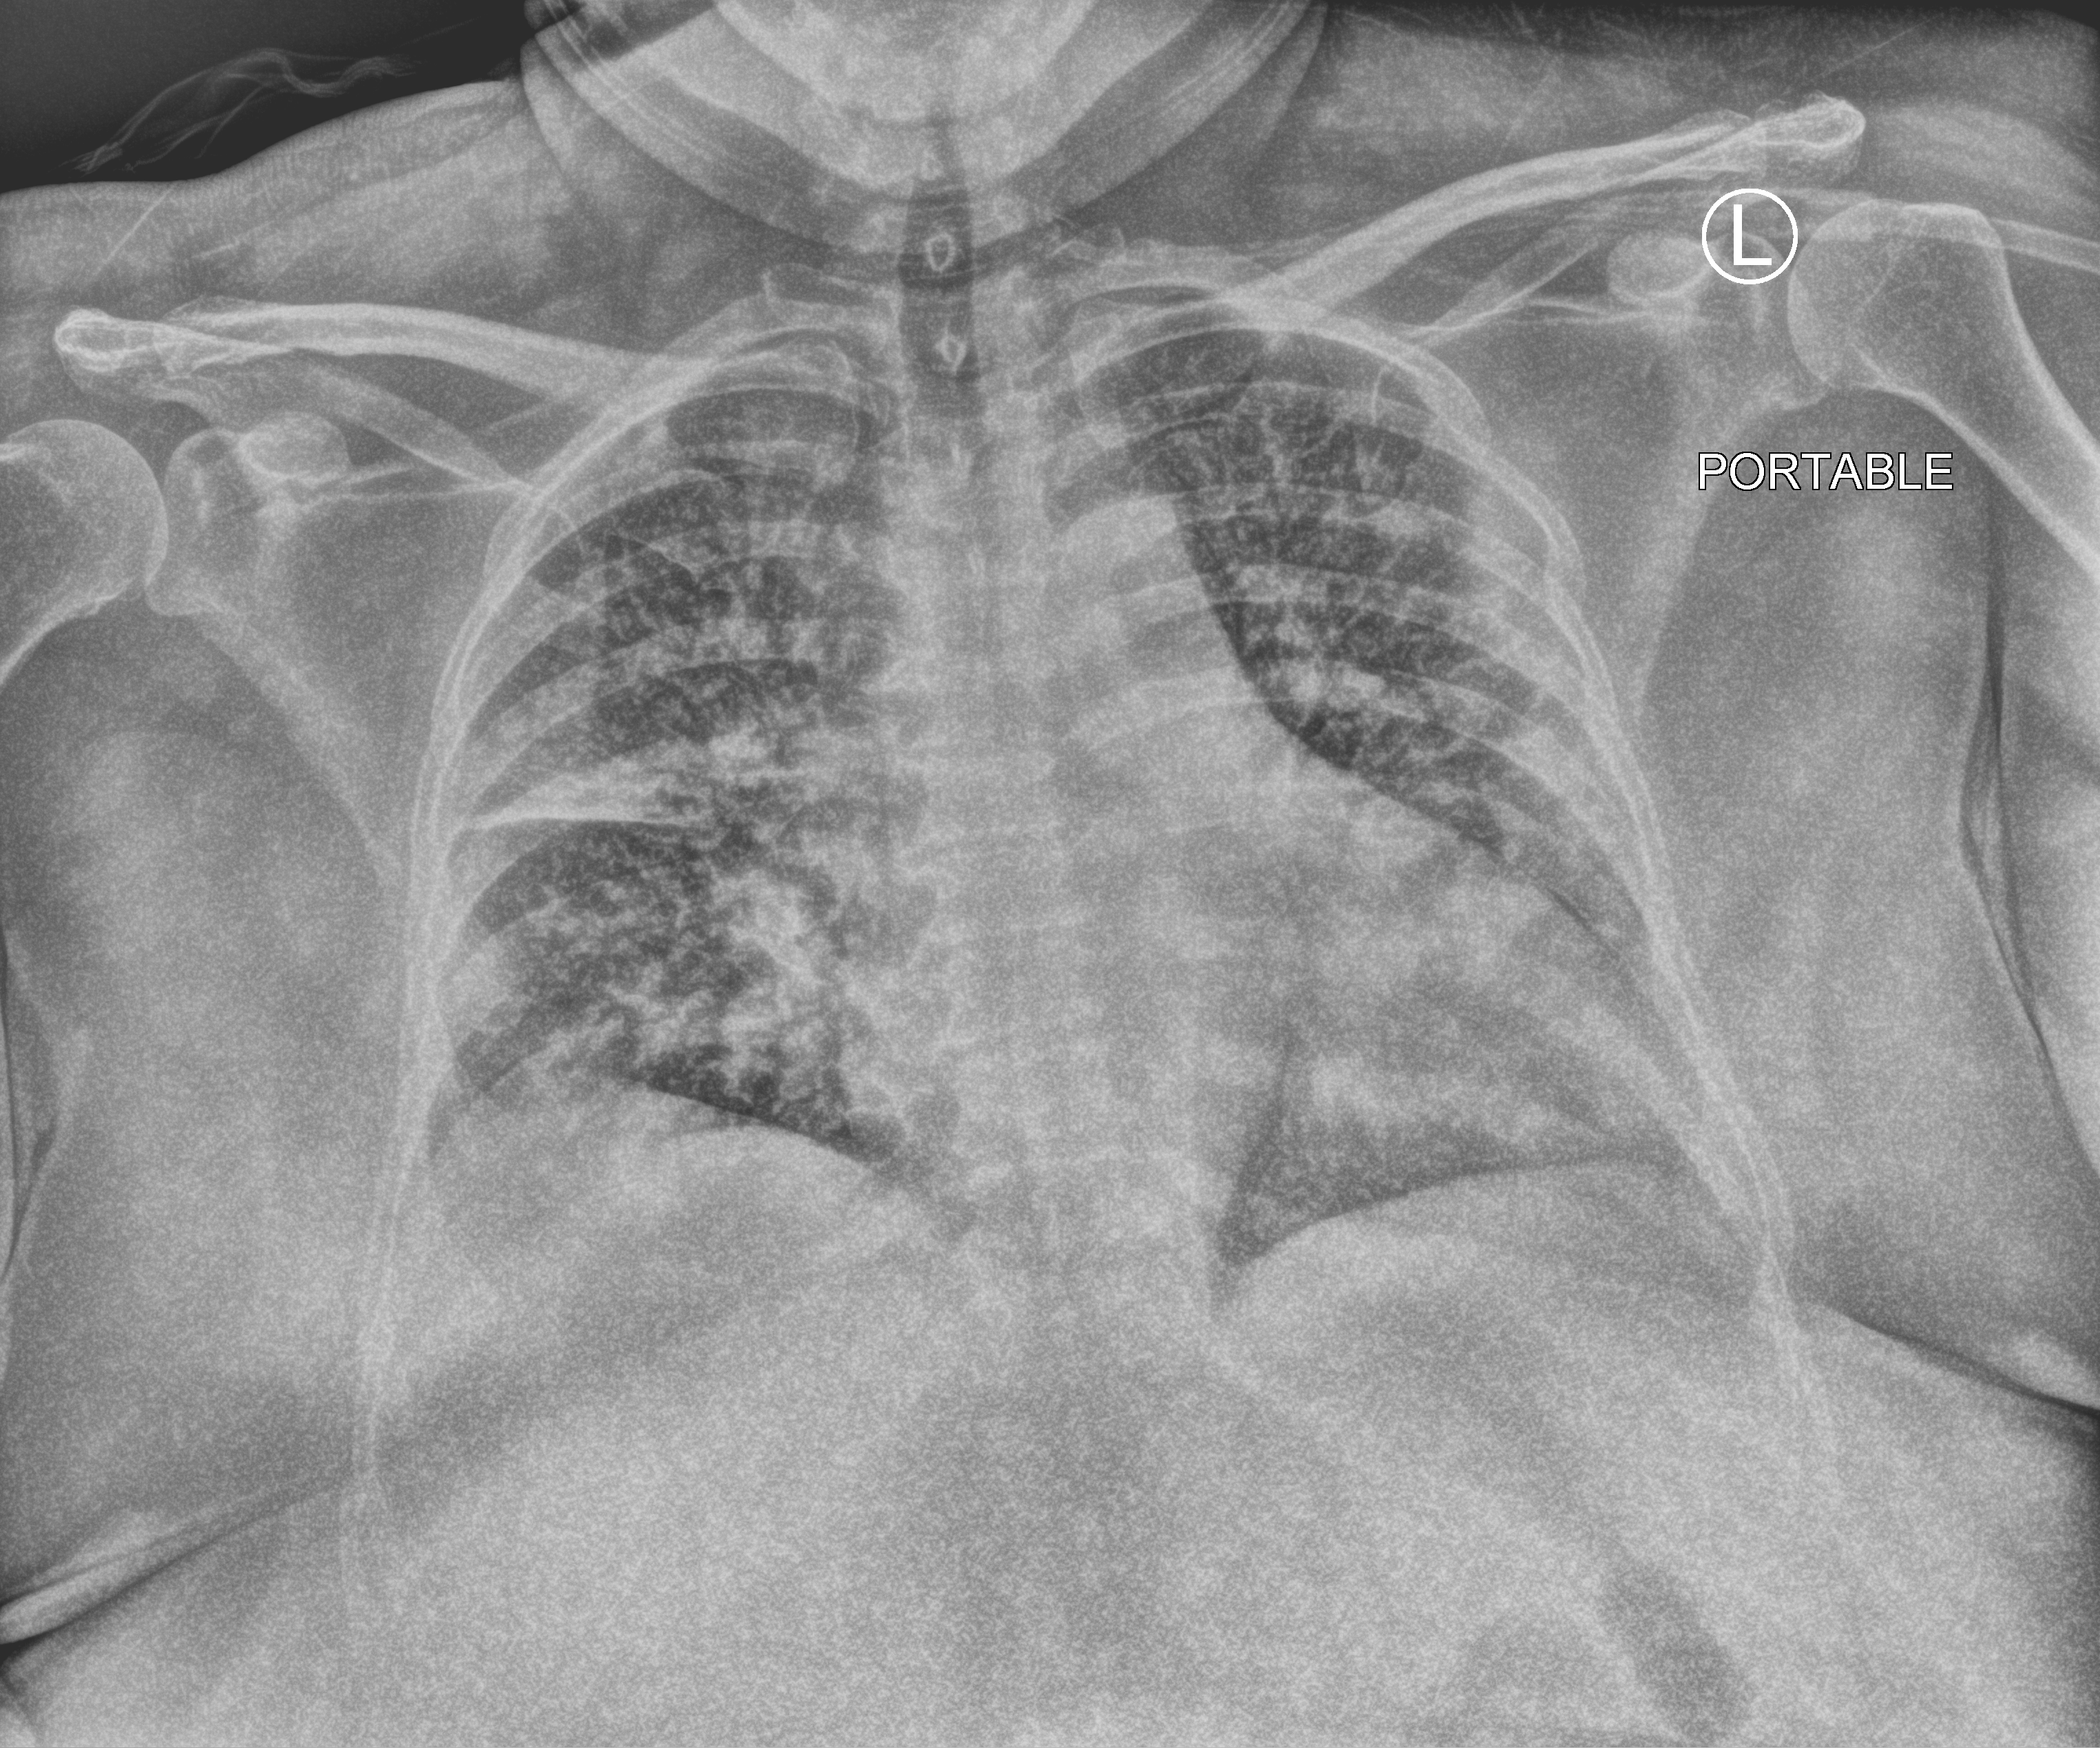
Portable chest radiograph, anteroposterior (AP) projection. Patient hospitalised with COVID-19; female, aged 60–74 years.
Admission-level facts for this patient (not findings on this image; timing relative to this image not recorded): other chronic lung disease (admission record): yes; admitted to intensive care during this hospital stay: no.